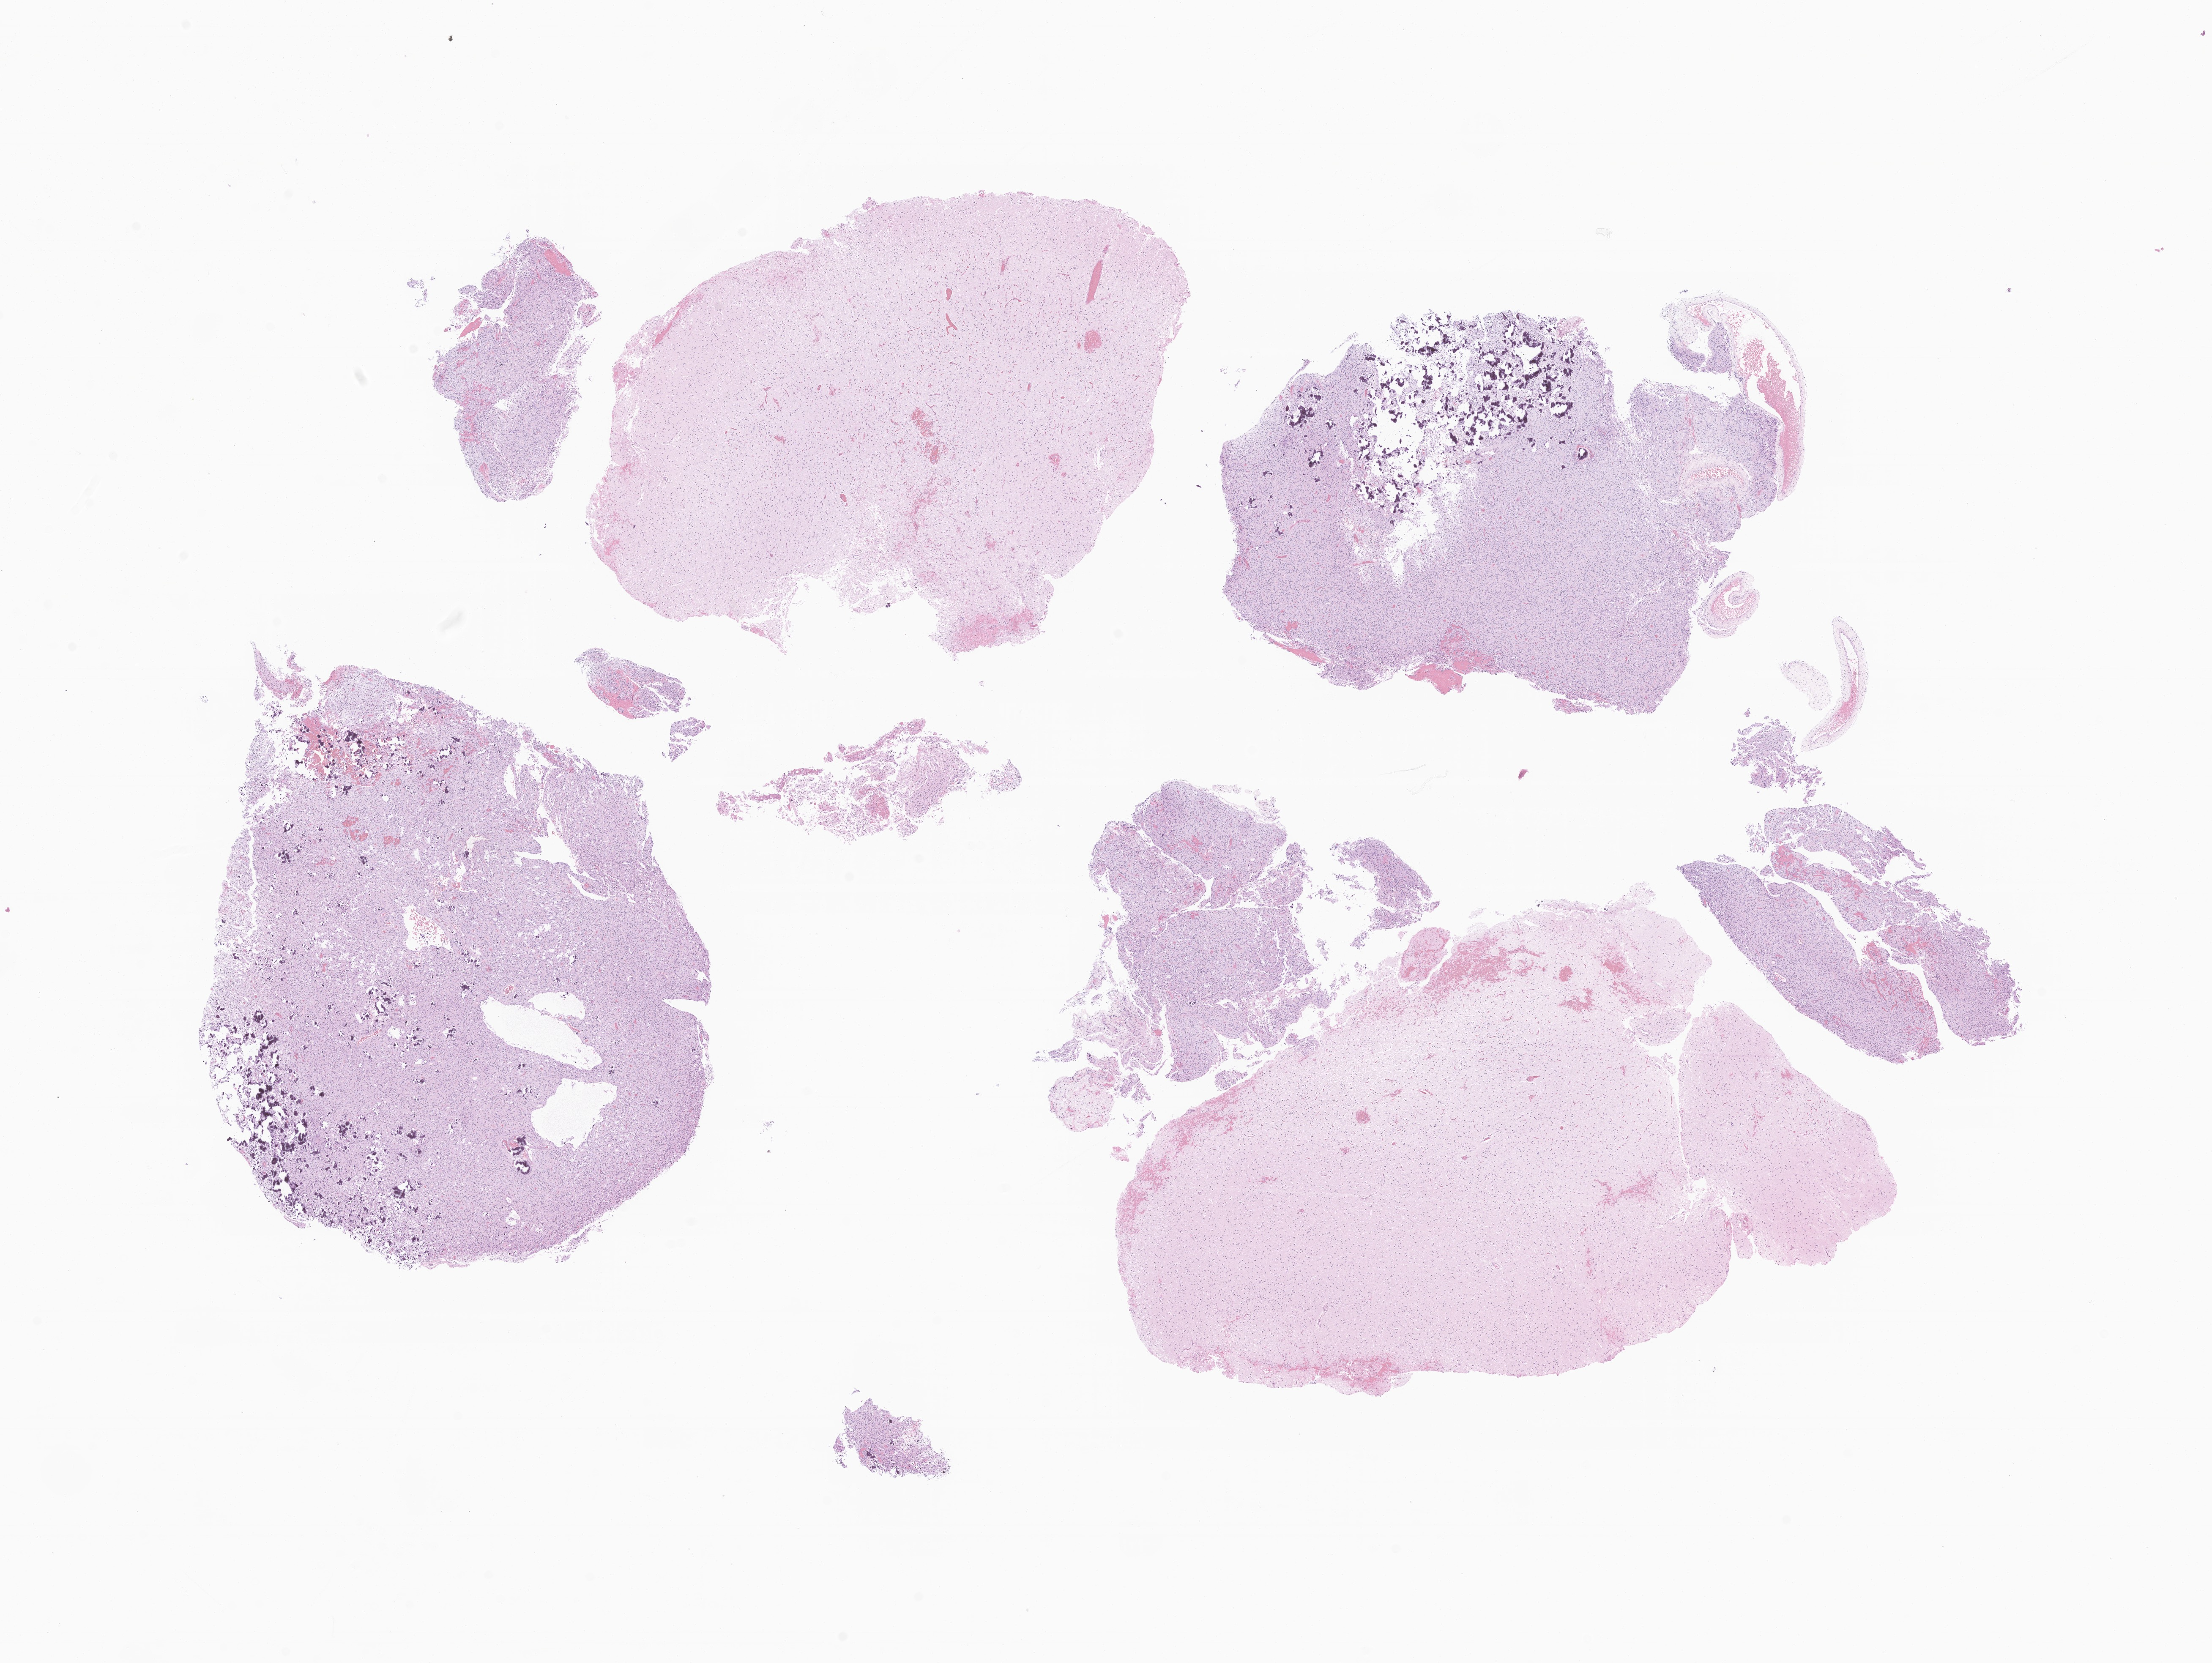
Digitized hematoxylin and eosin (H&E)-stained section of tumor tissue from the temporal lobe — whole scanned area (about 22.1 x 16.6 mm) shown as a low-resolution overview; formalin-fixed paraffin-embedded section. Patient: male, age 184 months.
Recorded diagnosis: Neuroepithelioma, NOS.